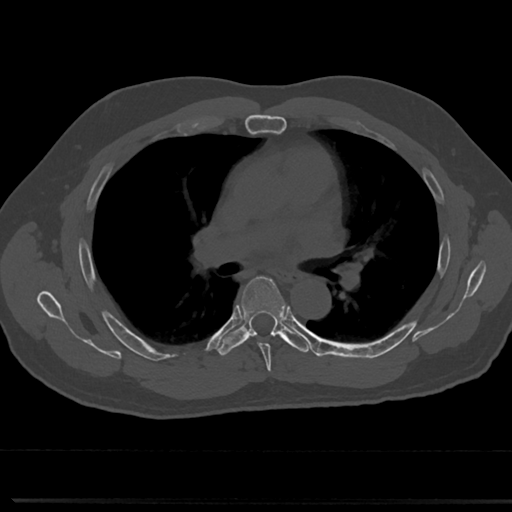
CT including the spine, one axial slice. Slice 470 of 817 in the series (ordered by position). 120 kVp. Bone window (W 1800 / L 400 HU). 0.5 mm slice thickness. 512 × 512 image matrix. Male patient, age 61 years. From the clinical record (not read from this slice): primary cancer: prostate.
Structures marked on this image (semi-automatic segmentation, software-assisted and operator-edited):
- T5 vertebra: bounding box (x1, y1, x2, y2) in pixels: (241, 277, 285, 362)
- T6 vertebra: (219, 275, 286, 354)